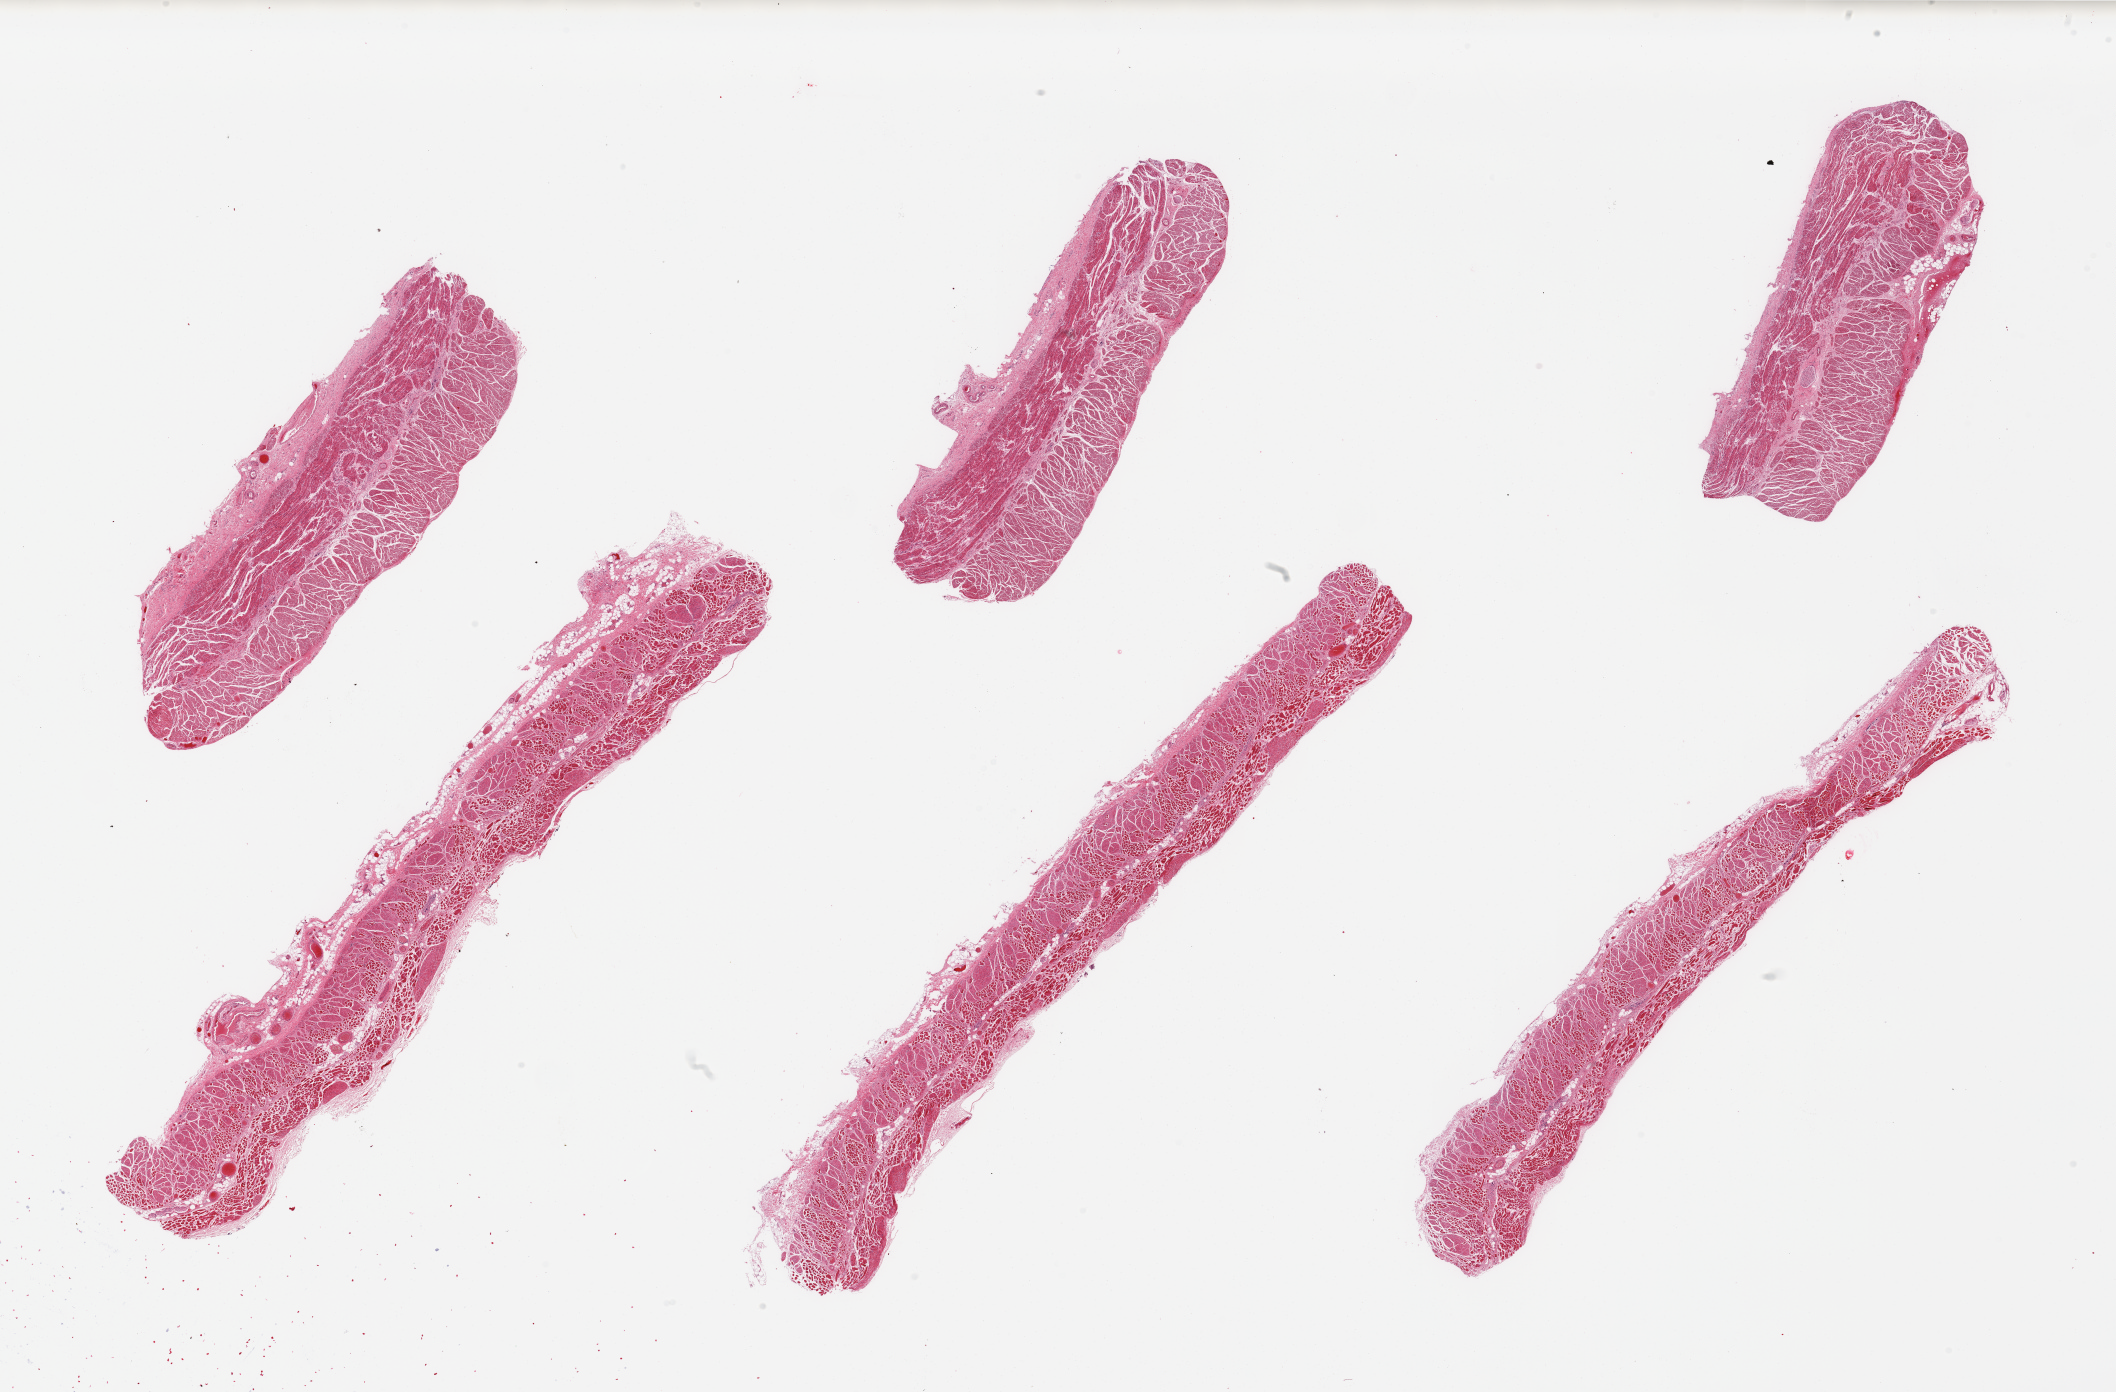
Whole-slide image, haematoxylin and eosin stain, brightfield, a low-resolution overview of the entire scanned area, about 33.5 x 22.0 mm, PAXgene-fixed paraffin-embedded (PFPE) section, sampled site (target tissue): esophageal muscle, tissue donor sample. Donor sex: male.
Reviewer comment on this tissue sample: 6 pieces; 3 of 6 include a significant portion of skeletal muscle admixed with smooth muscle indicating sampling too high.